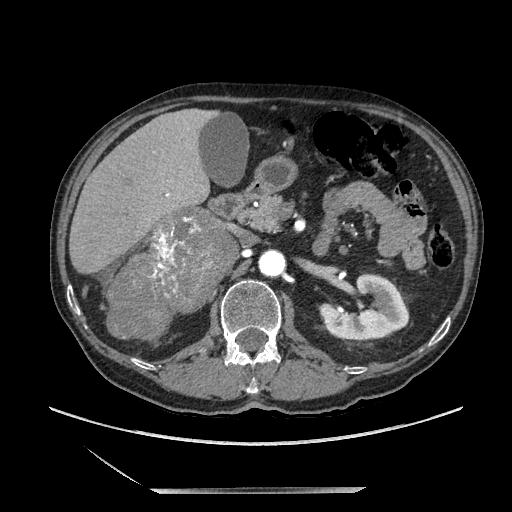
Contrast-enhanced abdominal CT, one axial slice. Position 106 of 243 along the scan axis. Soft-tissue window (W 400 / L 40 HU). 1.25 mm slice thickness. 512 × 512 image matrix. Male patient. Case-level facts recorded for this patient, not image findings: diagnosis: adrenocortical carcinoma; tumour side: right adrenal.
Outlined on this slice (semi-automatically segmented with operator editing):
- mass: bounding box (x1, y1, x2, y2) in pixels: (110, 208, 232, 339)